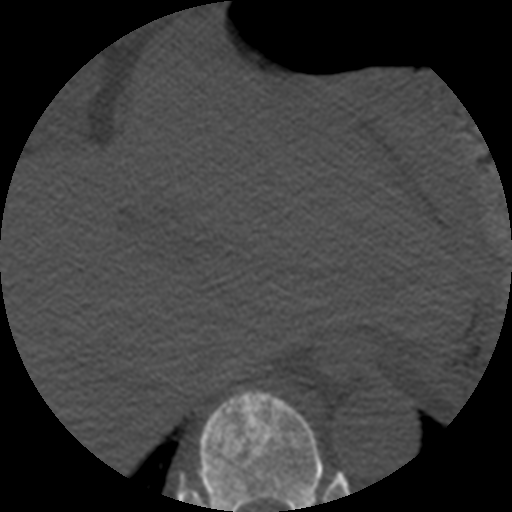
CT including the spine, one axial slice; slice 272 of 508 in the series (ordered by position); reconstruction kernel STANDARD; 120 kVp; bone window (W 1800 / L 400 HU); 512 × 512 image matrix, field of view 160 × 160 mm. Patient age 57 years. From the clinical record (not read from this slice): primary cancer: prostate.
Structures marked on this image (semi-automatically segmented with operator editing):
- T10 vertebra: bounding box (x1, y1, x2, y2) in pixels: (198, 390, 323, 512)
- T9 vertebra: (182, 475, 323, 501)